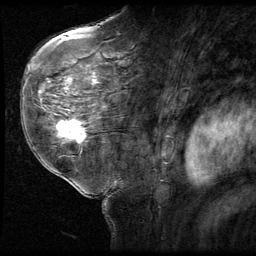
Breast MRI (dynamic contrast-enhanced), one sagittal slice. Position 38 of 58 along the scan axis. 3 images stored at this slice position (order not interpretable as contrast timing). 1.5 T. TE 4.2 ms, TR 9 ms. 2.5 mm slice thickness. 256 × 256 image matrix, field of view 180 × 180 mm. Patient: female, 58 years. Case-level facts recorded for this patient, not image findings: setting: breast cancer imaged before/during neoadjuvant chemotherapy; receptor status: HR-positive, HER2-negative.
Annotated regions visible in this slice (semi-automatically segmented with operator editing):
- analysis volume of interest (the breast-tissue region the enhancement analysis was run in; not a lesion): bounding box [x1, y1, x2, y2] px = [51, 116, 93, 151]
- tumour enhancement mask (voxels above the 140 % enhancement threshold inside the analysis volume of interest): [57, 120, 86, 143]